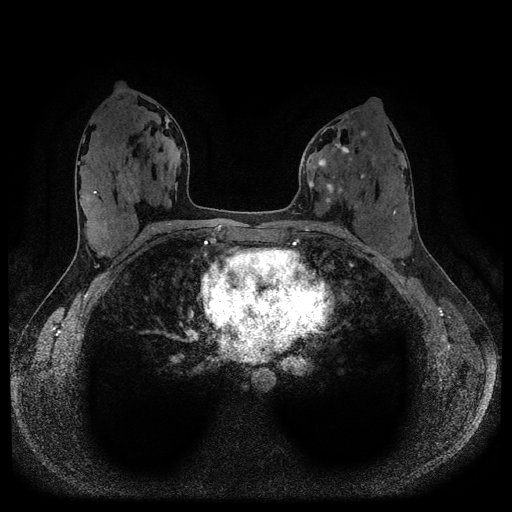
Breast MRI (dynamic contrast-enhanced, multi-phase), one axial slice. Slice 51 of 116 in the series (ordered by position). Dynamic contrast-enhanced series, time point 2 of 5 at this slice position (early post-contrast). 1.5 T. TE 2.6 ms, TR 5.3 ms. 2 mm slice thickness. 512 × 512 image matrix, field of view 350 × 350 mm. Female patient, age 33 years.
Outlined on this slice (semi-automatic segmentation, software-assisted and operator-edited):
- breast lesion (labelled 'tumour' in the annotation; benign lesions carry a separate 'benign' label): box from (x=308, y=143) to (x=365, y=204) px